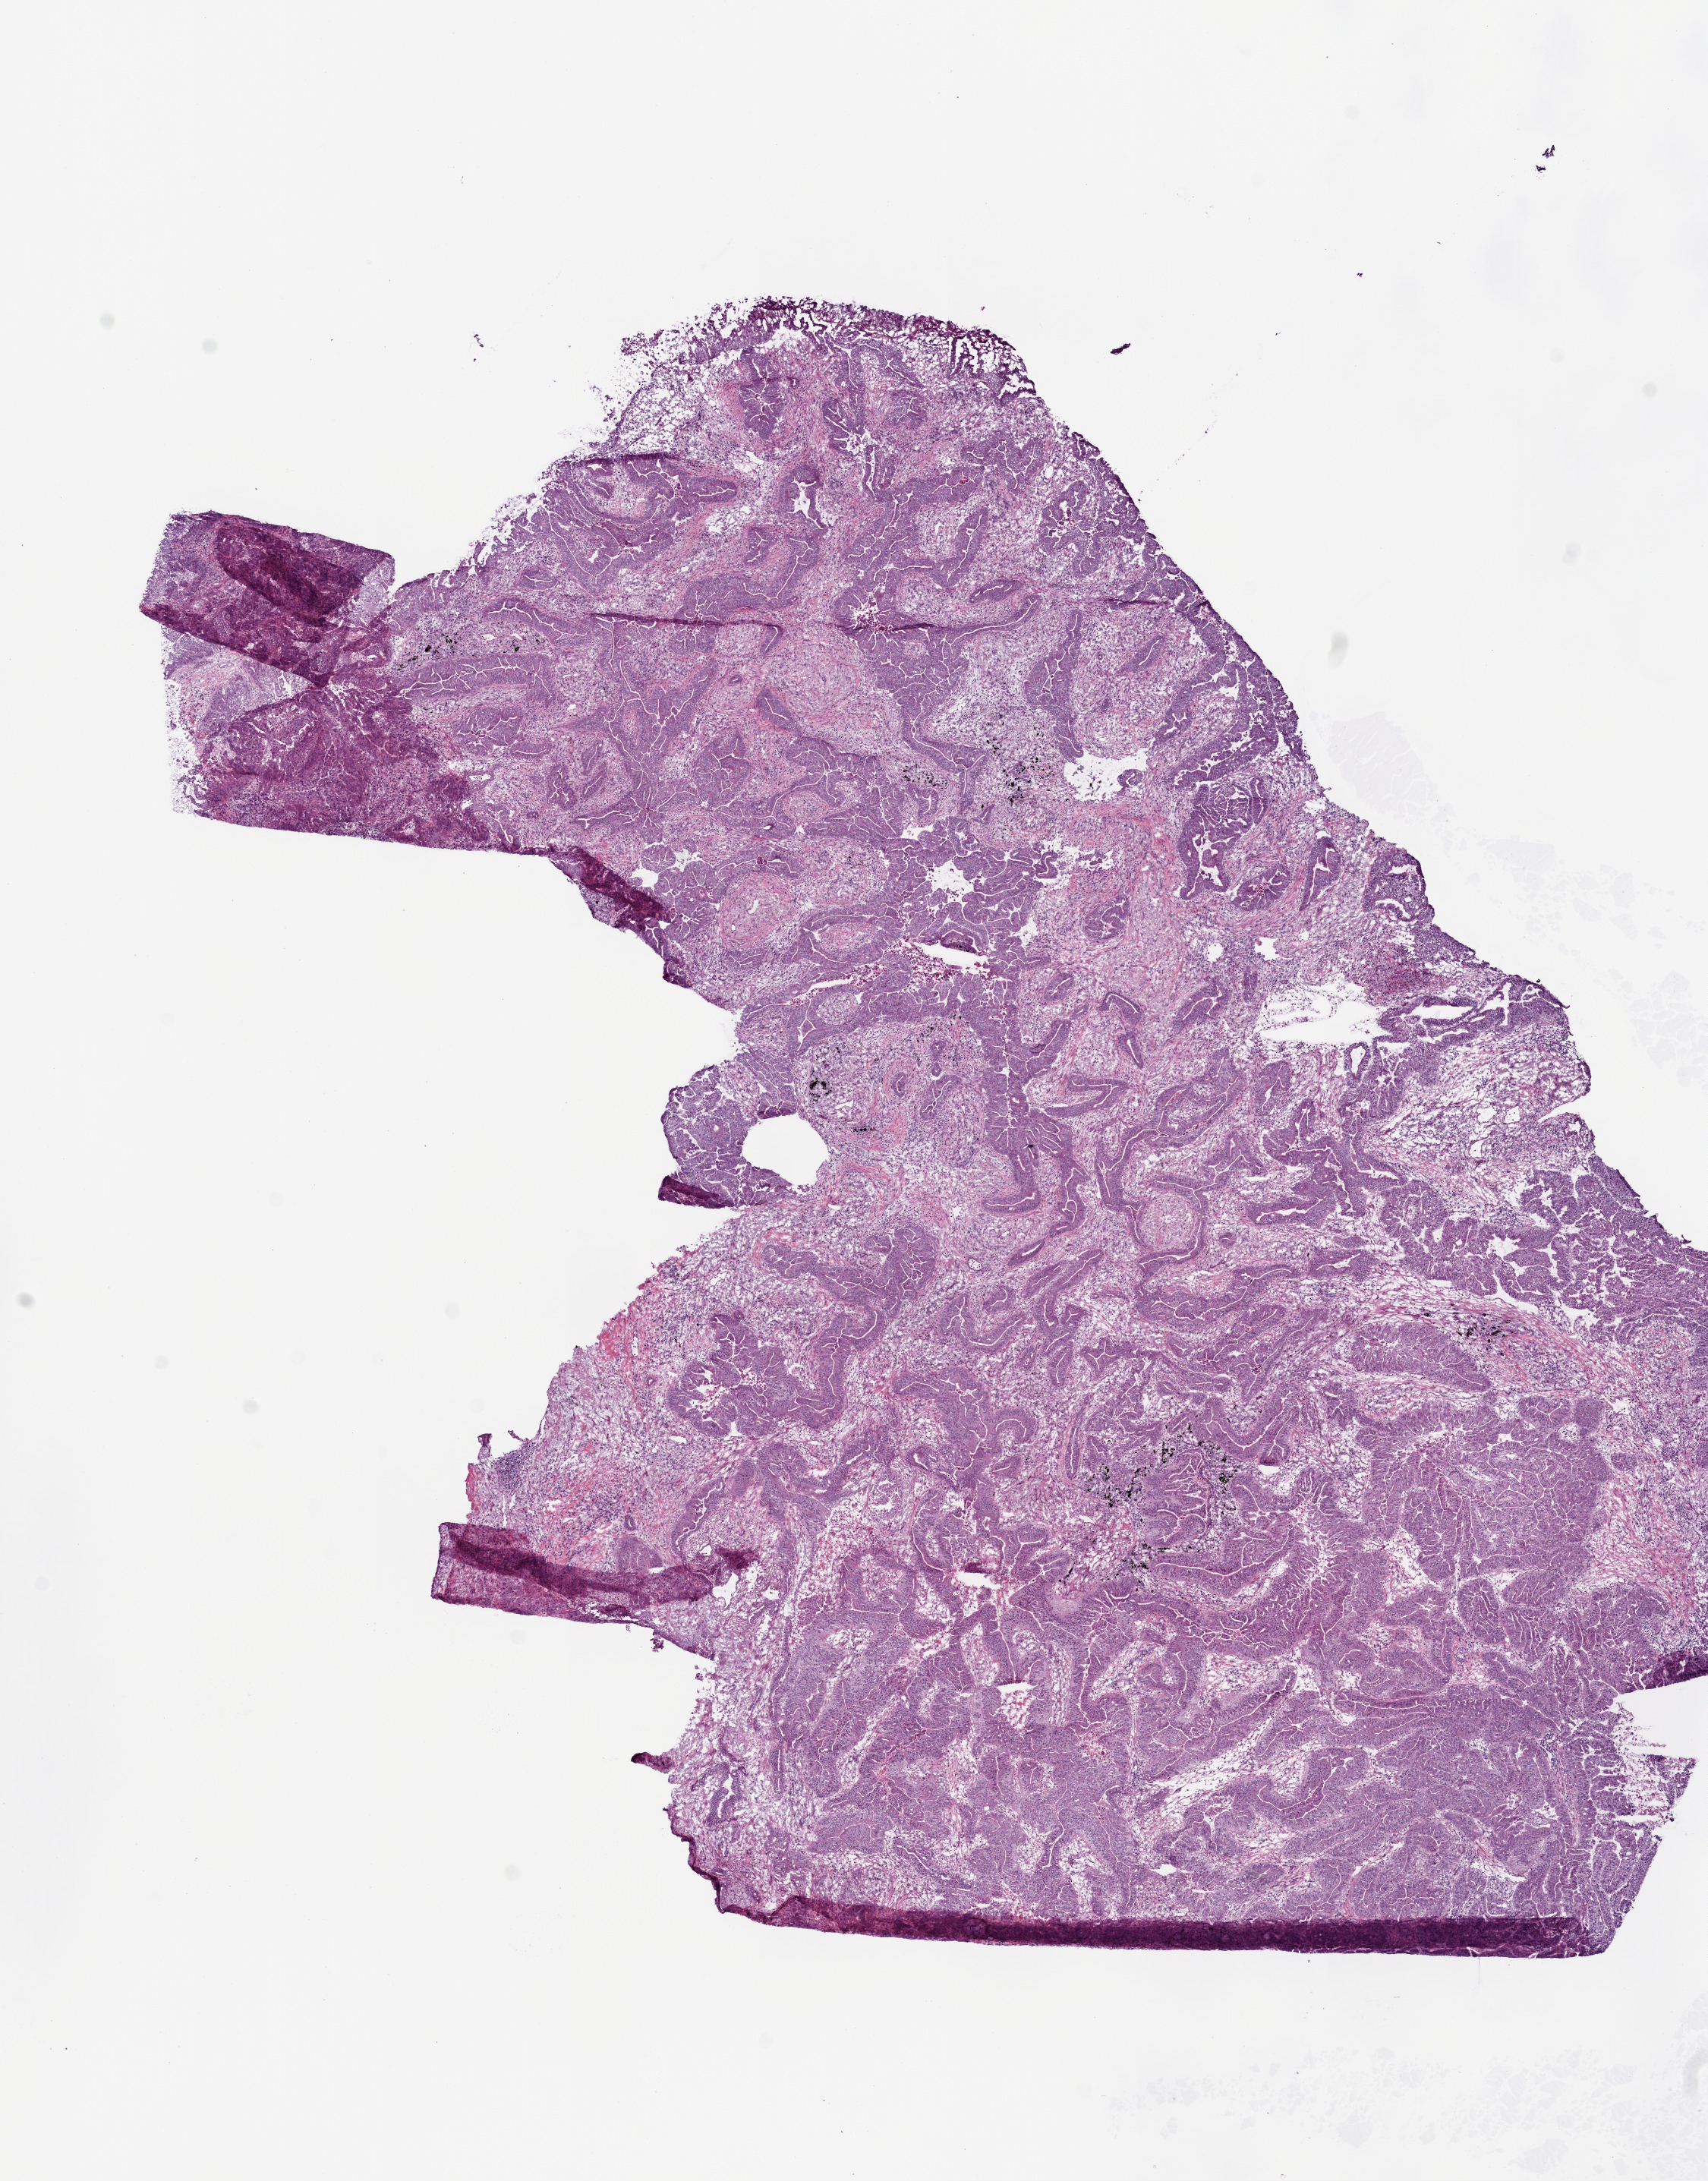
H&E-stained whole-slide image — low-resolution overview of the scanned area, about 9.0 x 11.5 mm; frozen section from the top of the tissue portion; sample: primary tumour, lung. Male patient; age at initial diagnosis 60 years. Slide review estimates, as recorded: tumour cells 100%, tumour nuclei 80%, normal cells 0%, stromal cells 0%, necrosis 0%. Infiltration values recorded for this section: lymphocyte infiltration 5%, monocyte infiltration 1%, neutrophil infiltration 5%.
- diagnosis: Adenocarcinoma, NOS
- AJCC pathologic stage: IIIA (7th edition)
- laterality: left